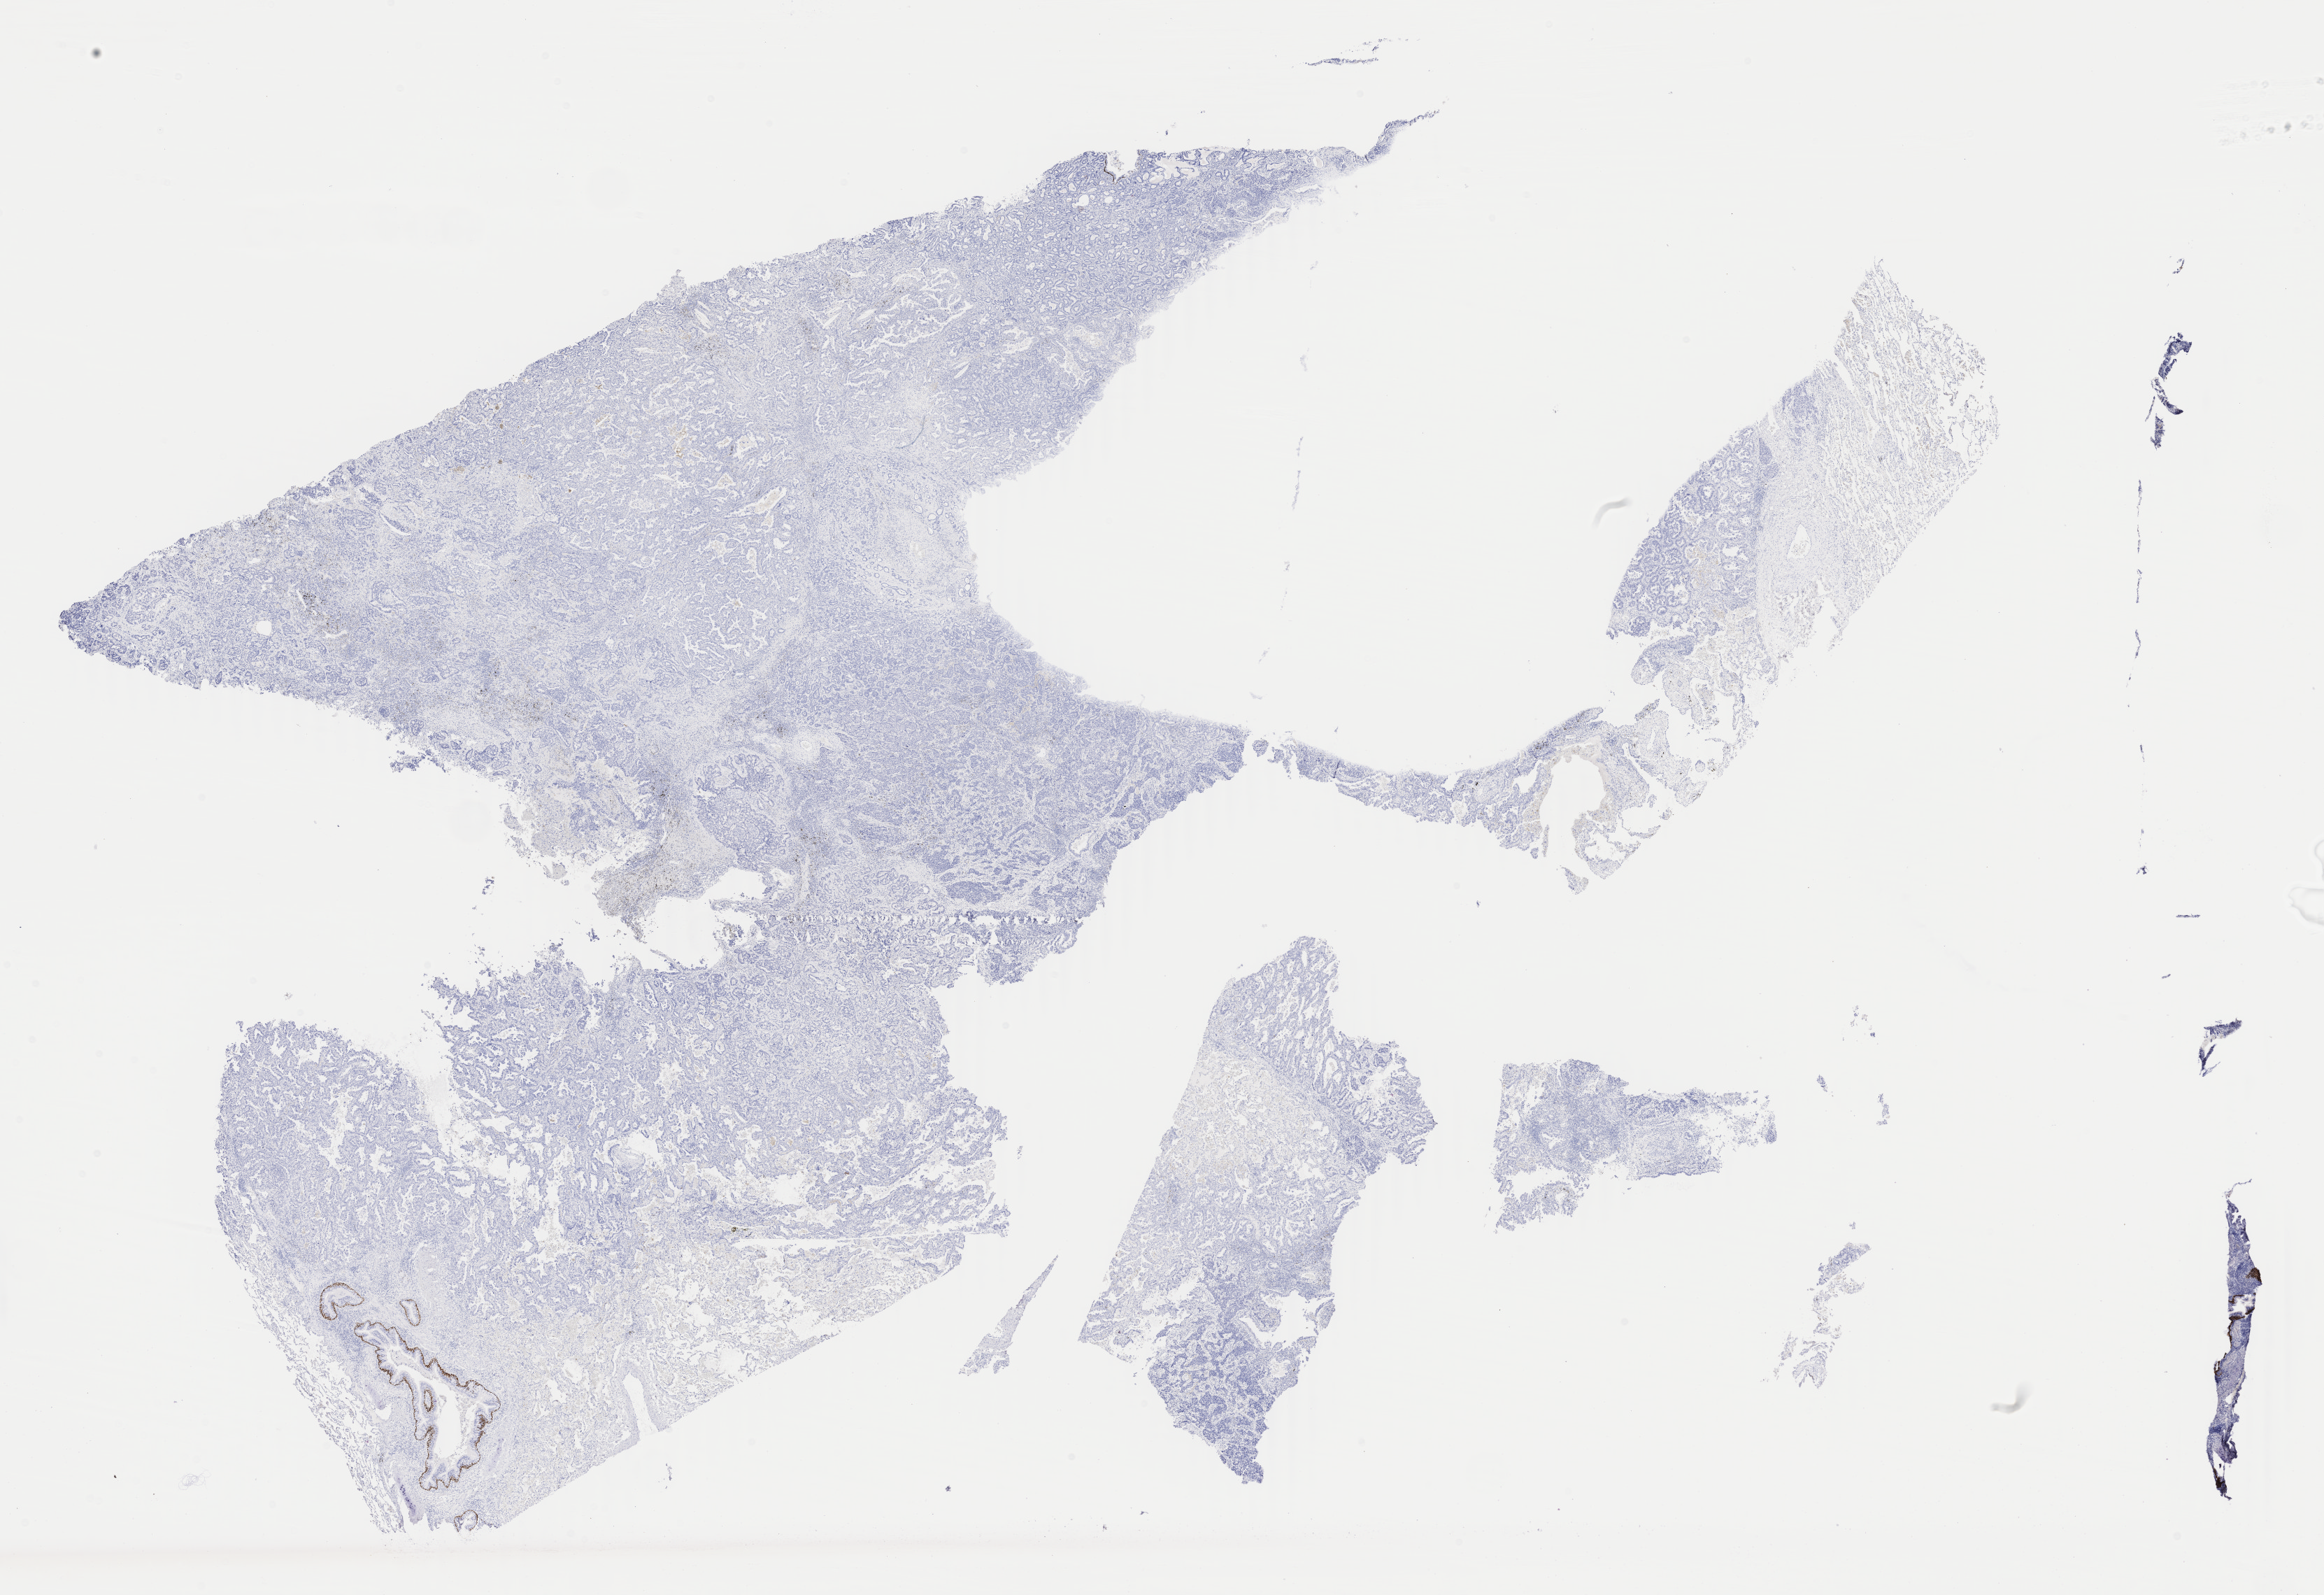
IHC for p40, whole-slide image — a low-resolution overview of the entire scanned area, about 26.4 x 18.1 mm; tumor tissue; site: lung (right). Patient: male, aged 51.
Histologic diagnosis: Adenocarcinoma, NOS.